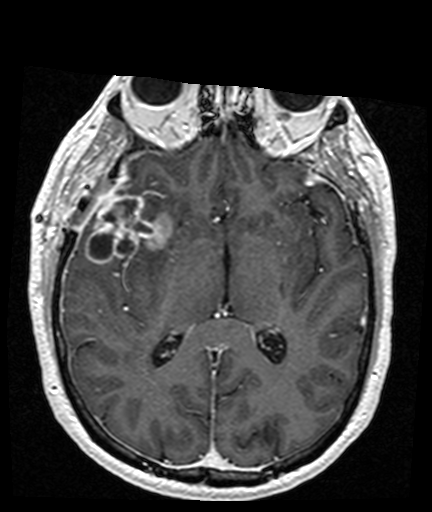
Brain MRI from a brain-tumour surgery series, one axial slice. Position 87 of 176 along the scan axis. T1-weighted post-contrast. 1 mm slice thickness. 432 × 512 image matrix, field of view 194 × 230 mm. Case-level facts recorded for this patient, not image findings: histopathology: Glioblastoma; WHO grade: 4; IDH mutation: no; tumour location: Right Frontal Temporal, Posterior Sylvian Fissure.
Annotated regions visible in this slice (outlined manually by an expert reader):
- tumour: bounding box (x1, y1, x2, y2) in pixels: (85, 189, 170, 264)